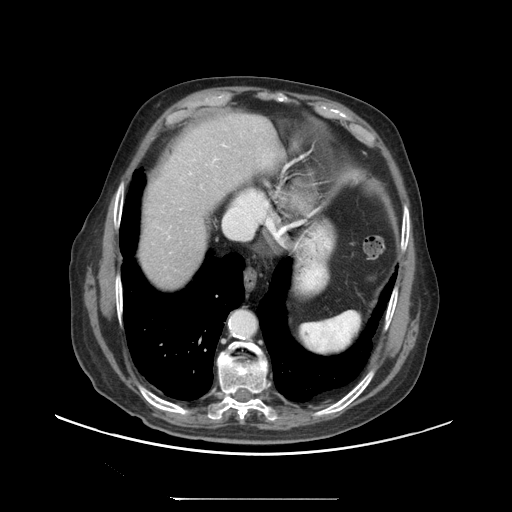
Contrast-enhanced abdominal CT (liver protocol), one axial slice; slice 84 of 97 in the series (ordered by position); reconstruction kernel STANDARD; soft-tissue window (W 400 / L 40 HU); 2.5 mm slice thickness; 512 × 512 image matrix. From the clinical record (not read from this slice): diagnosis: hepatocellular carcinoma (patient treated with transarterial chemoembolisation; whether this scan precedes or follows treatment is not stated here); TNM stage (as recorded): Stage-IIIC; Child-Pugh class: A; tumour differentiation: well differentiated; tumour nodularity: uninodular.
Outlined on this slice (semi-automatically segmented with operator editing):
- abdominal aorta: bounding box <231,310,256,337> (left, top, right, bottom; pixels)
- liver parenchyma outside the tumour (the mass and vessels are separate outlines, so this box may not span the whole liver): <140,114,280,288>
- liver vessels: <189,144,225,174>